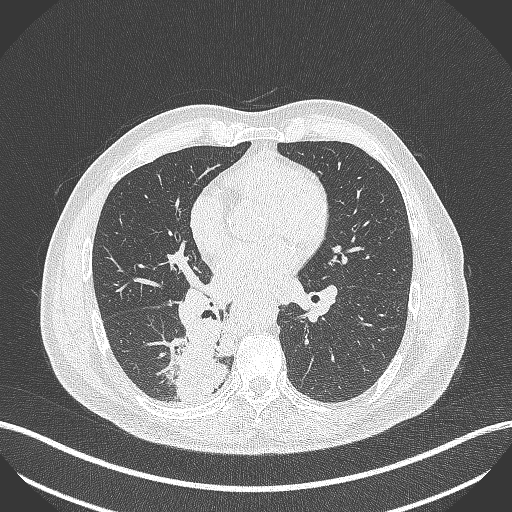
Chest CT, one axial slice. Slice 226 of 451 in the series (ordered by position). Reconstruction kernel B70f. 100 kVp. Lung window (W 1500 / L -600 HU). 1 mm slice thickness. 512 × 512 image matrix, field of view 400 × 400 mm. Patient: male, 61 years. From the clinical record (not read from this slice): clinical TNM (as recorded): T1 N0 M0.
Structures marked on this image (bounding box drawn by a radiologist):
- lung tumour (recorded histology: small cell carcinoma): bounding box <164,320,229,401> (left, top, right, bottom; pixels)